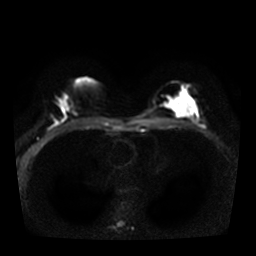
Breast MRI, one axial slice. Slice 18 of 36 in the series (ordered by position). Diffusion-weighted series; image 2 of 4 stored at this slice position (different b-values; order by instance number). 3 T. 5 mm slice thickness. 256 × 256 image matrix, field of view 320 × 320 mm. Female patient.
Annotated regions visible in this slice (outlined manually by an expert reader):
- tumour on diffusion-weighted imaging: bounding box <169,91,197,117> (left, top, right, bottom; pixels)